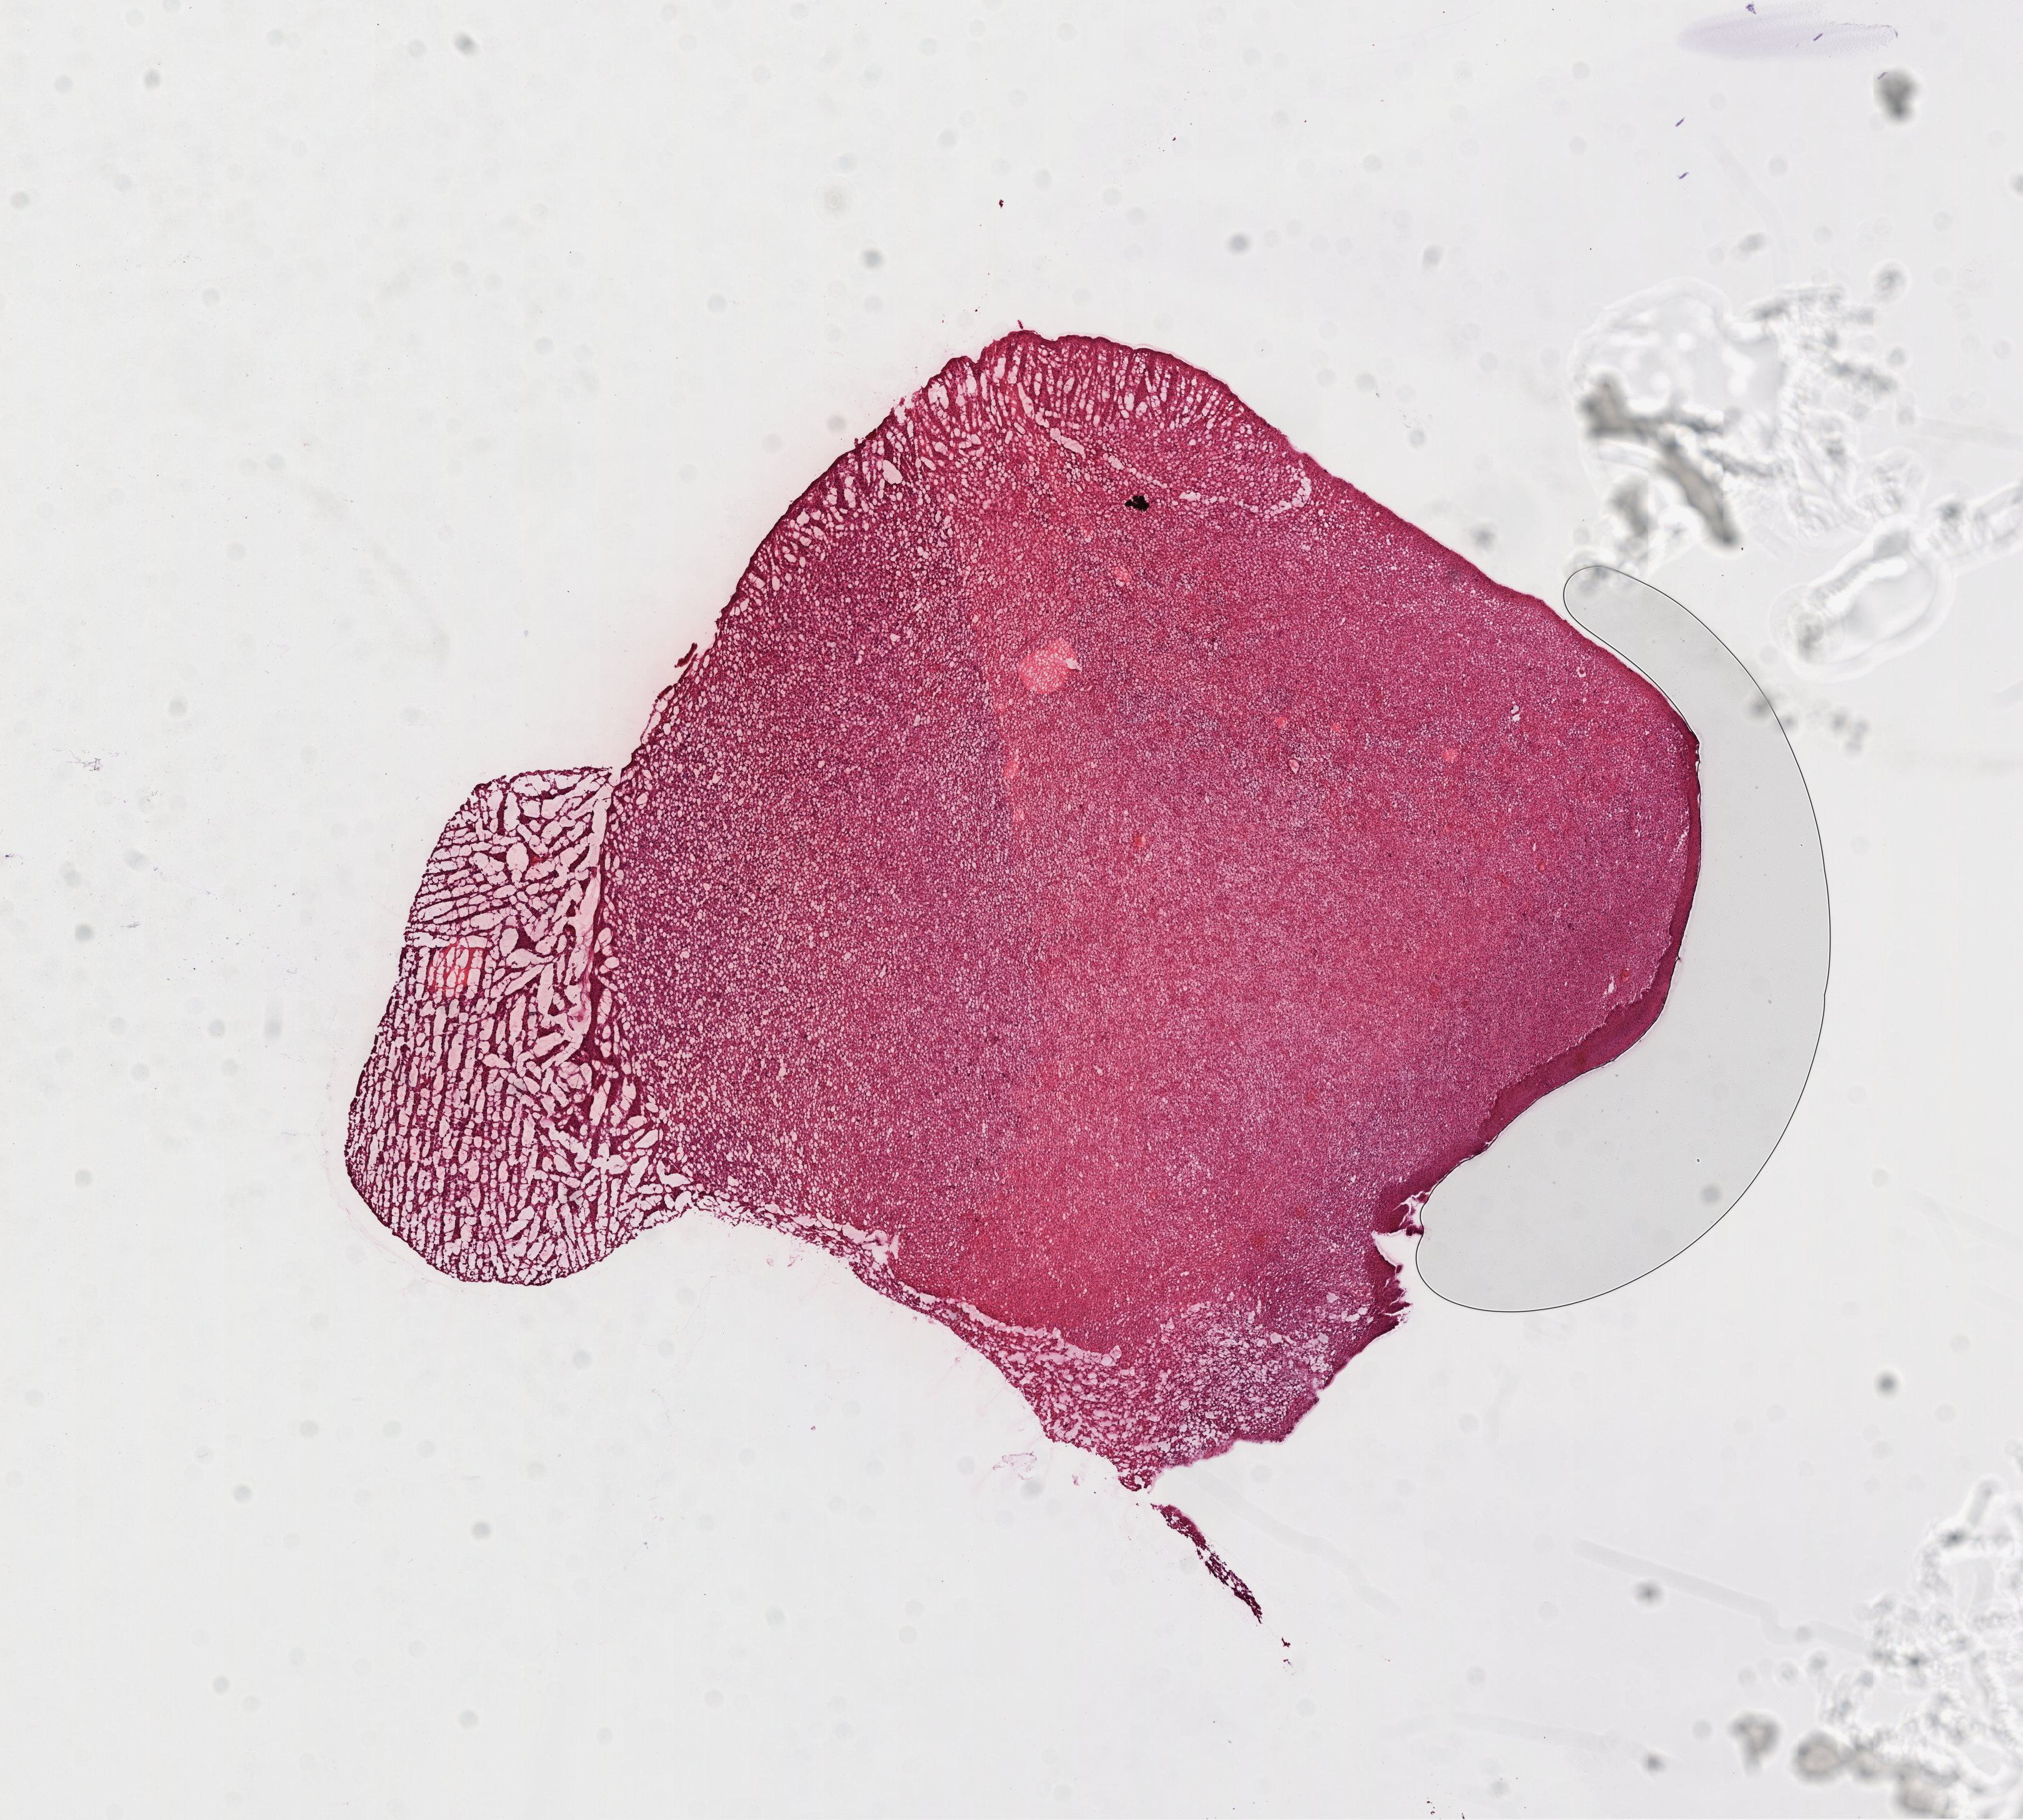
Hematoxylin and eosin (H&E) stained whole-slide image — shown as a low-resolution overview of the whole scanned area (about 13.1 x 11.7 mm, from a 20x scan). Frozen section. Brain, primary tumour sample. Male, age 63 years at initial diagnosis. Pathologist review of this section (percent, as recorded): tumour cells 100%, tumour nuclei 100%, normal cells 0%, stromal cells 0%, necrosis 0%.
• diagnosis: Glioblastoma